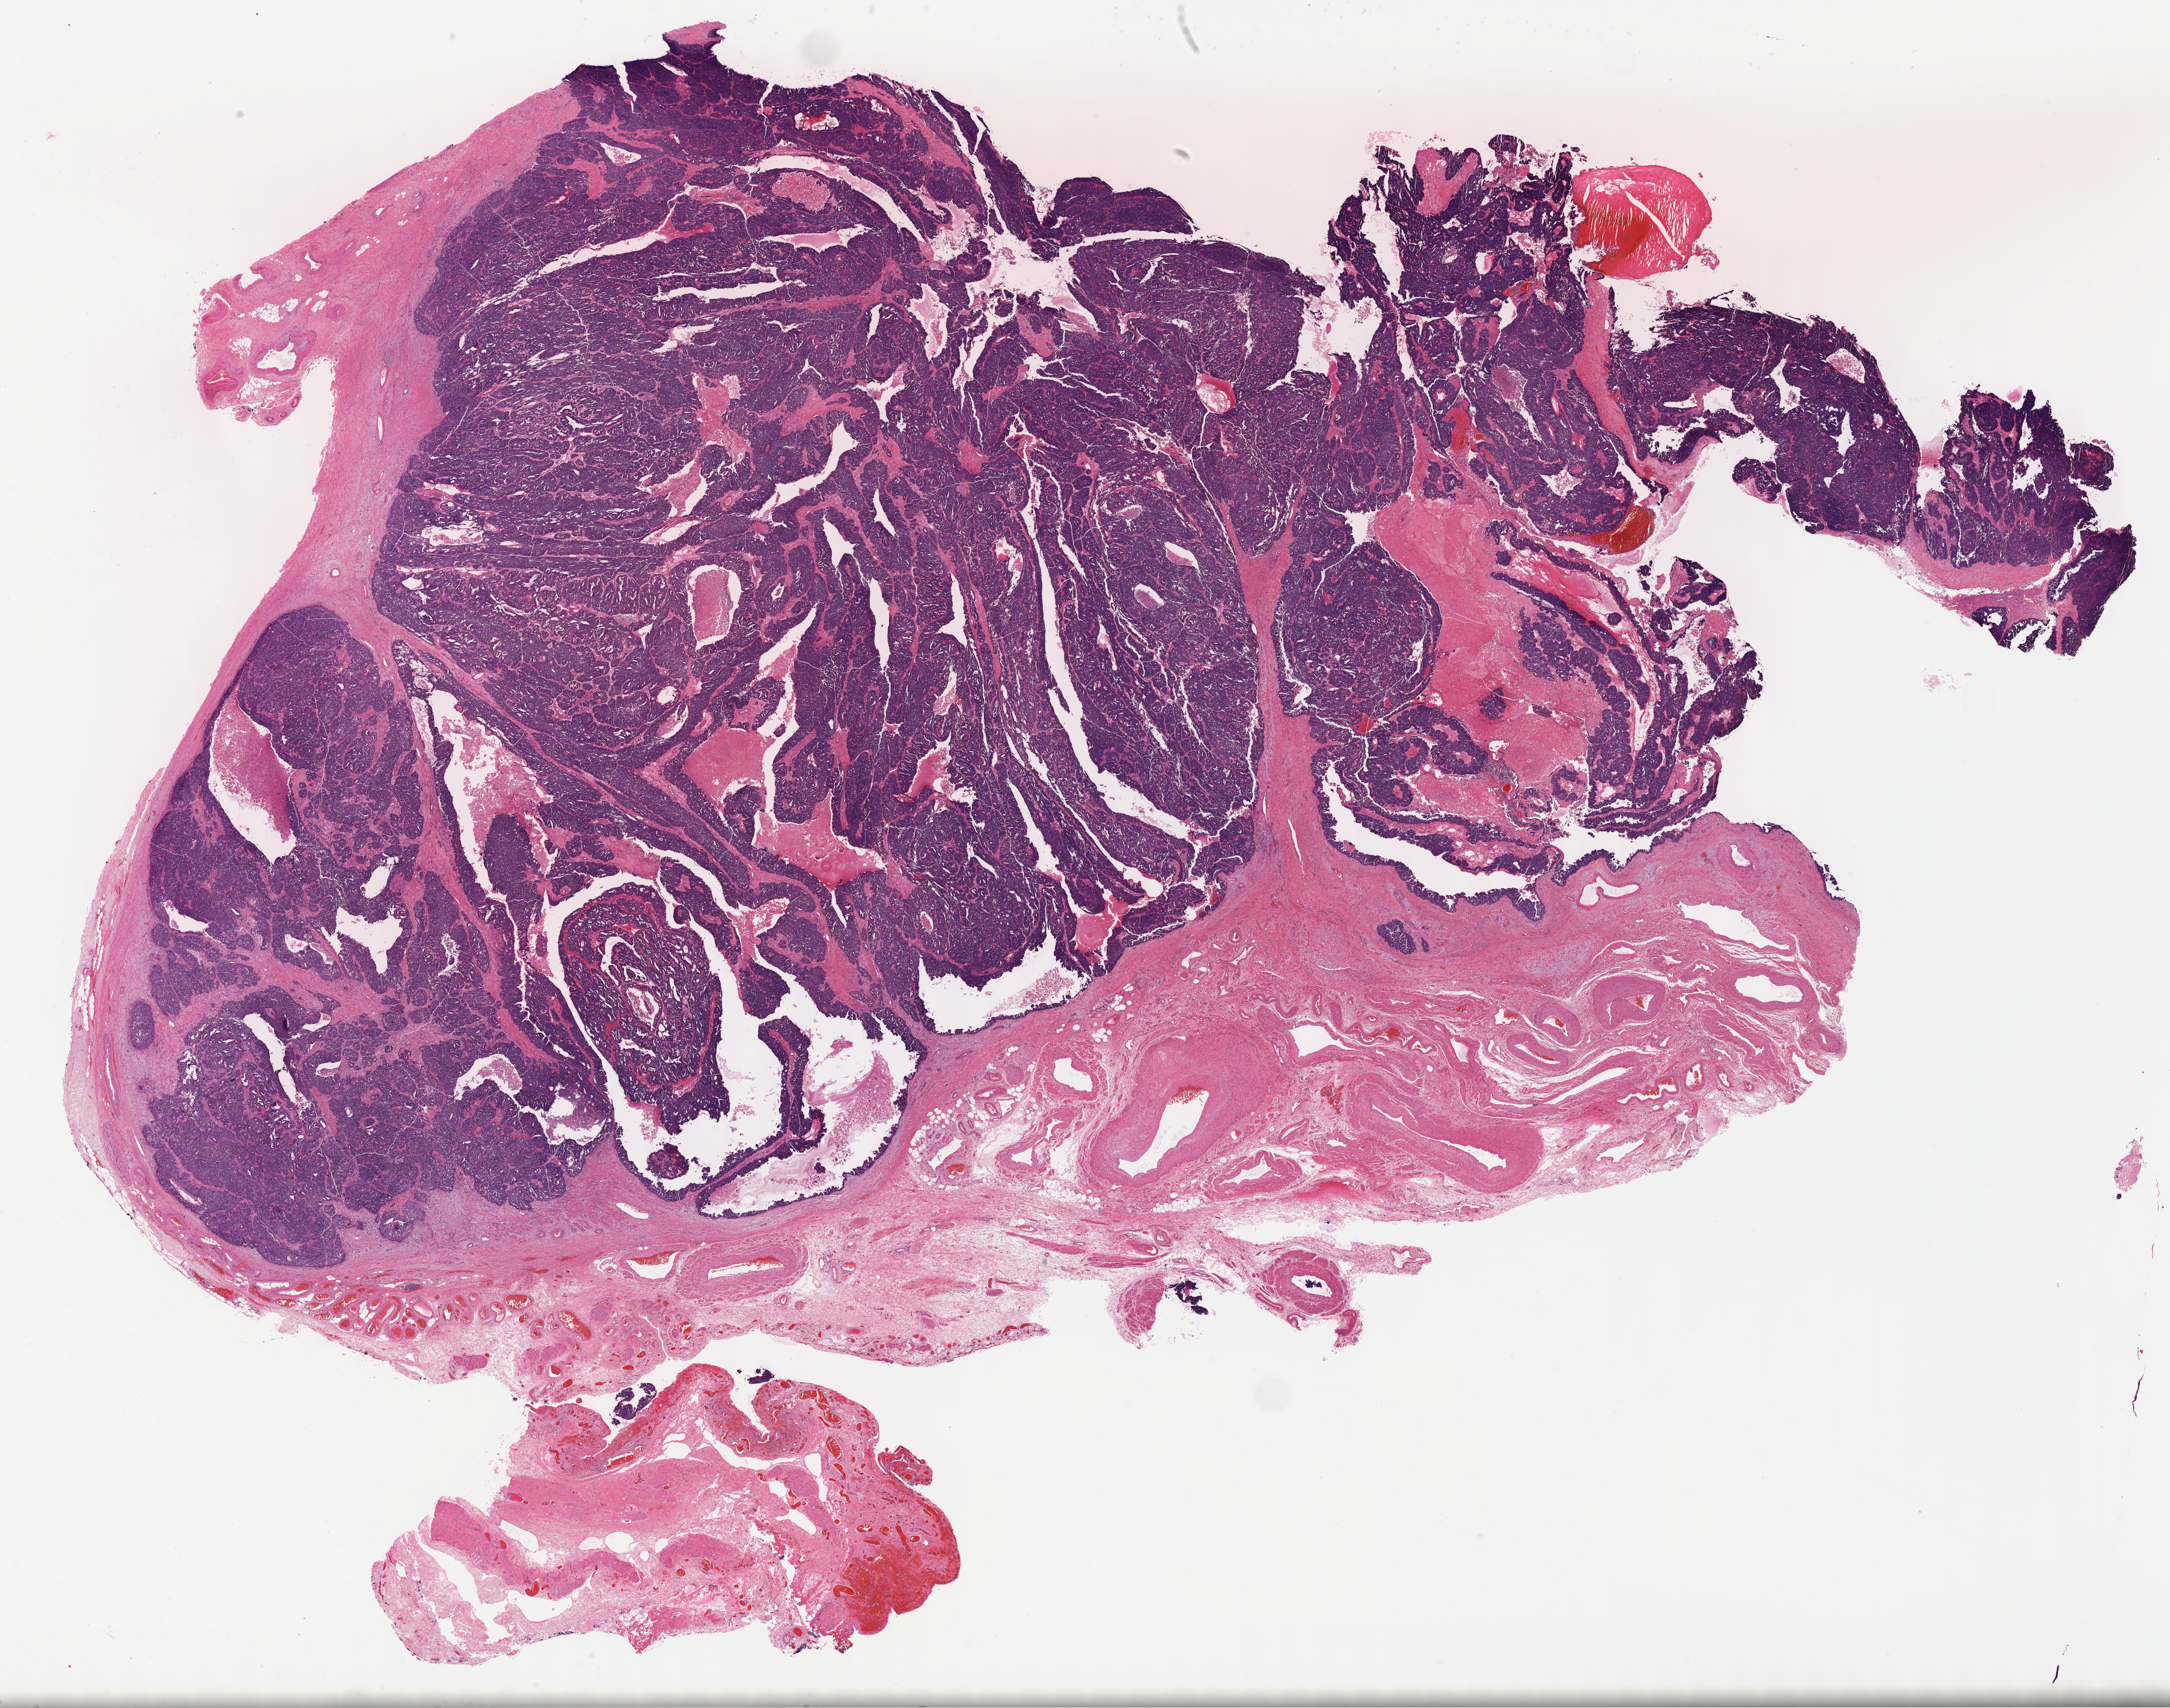
Whole-slide histology image, H&E-stained, whole scanned area (about 29.2 x 23.0 mm, from a 40x scan) shown as a low-resolution overview, formalin-fixed paraffin-embedded (FFPE) diagnostic section, primary tumour sample from the ovary. Female, age 62 years at initial diagnosis. Histologic grade: G3 (poorly differentiated).
Pathologic diagnosis: Serous cystadenocarcinoma, NOS. FIGO stage: IIIC. Laterality: right.